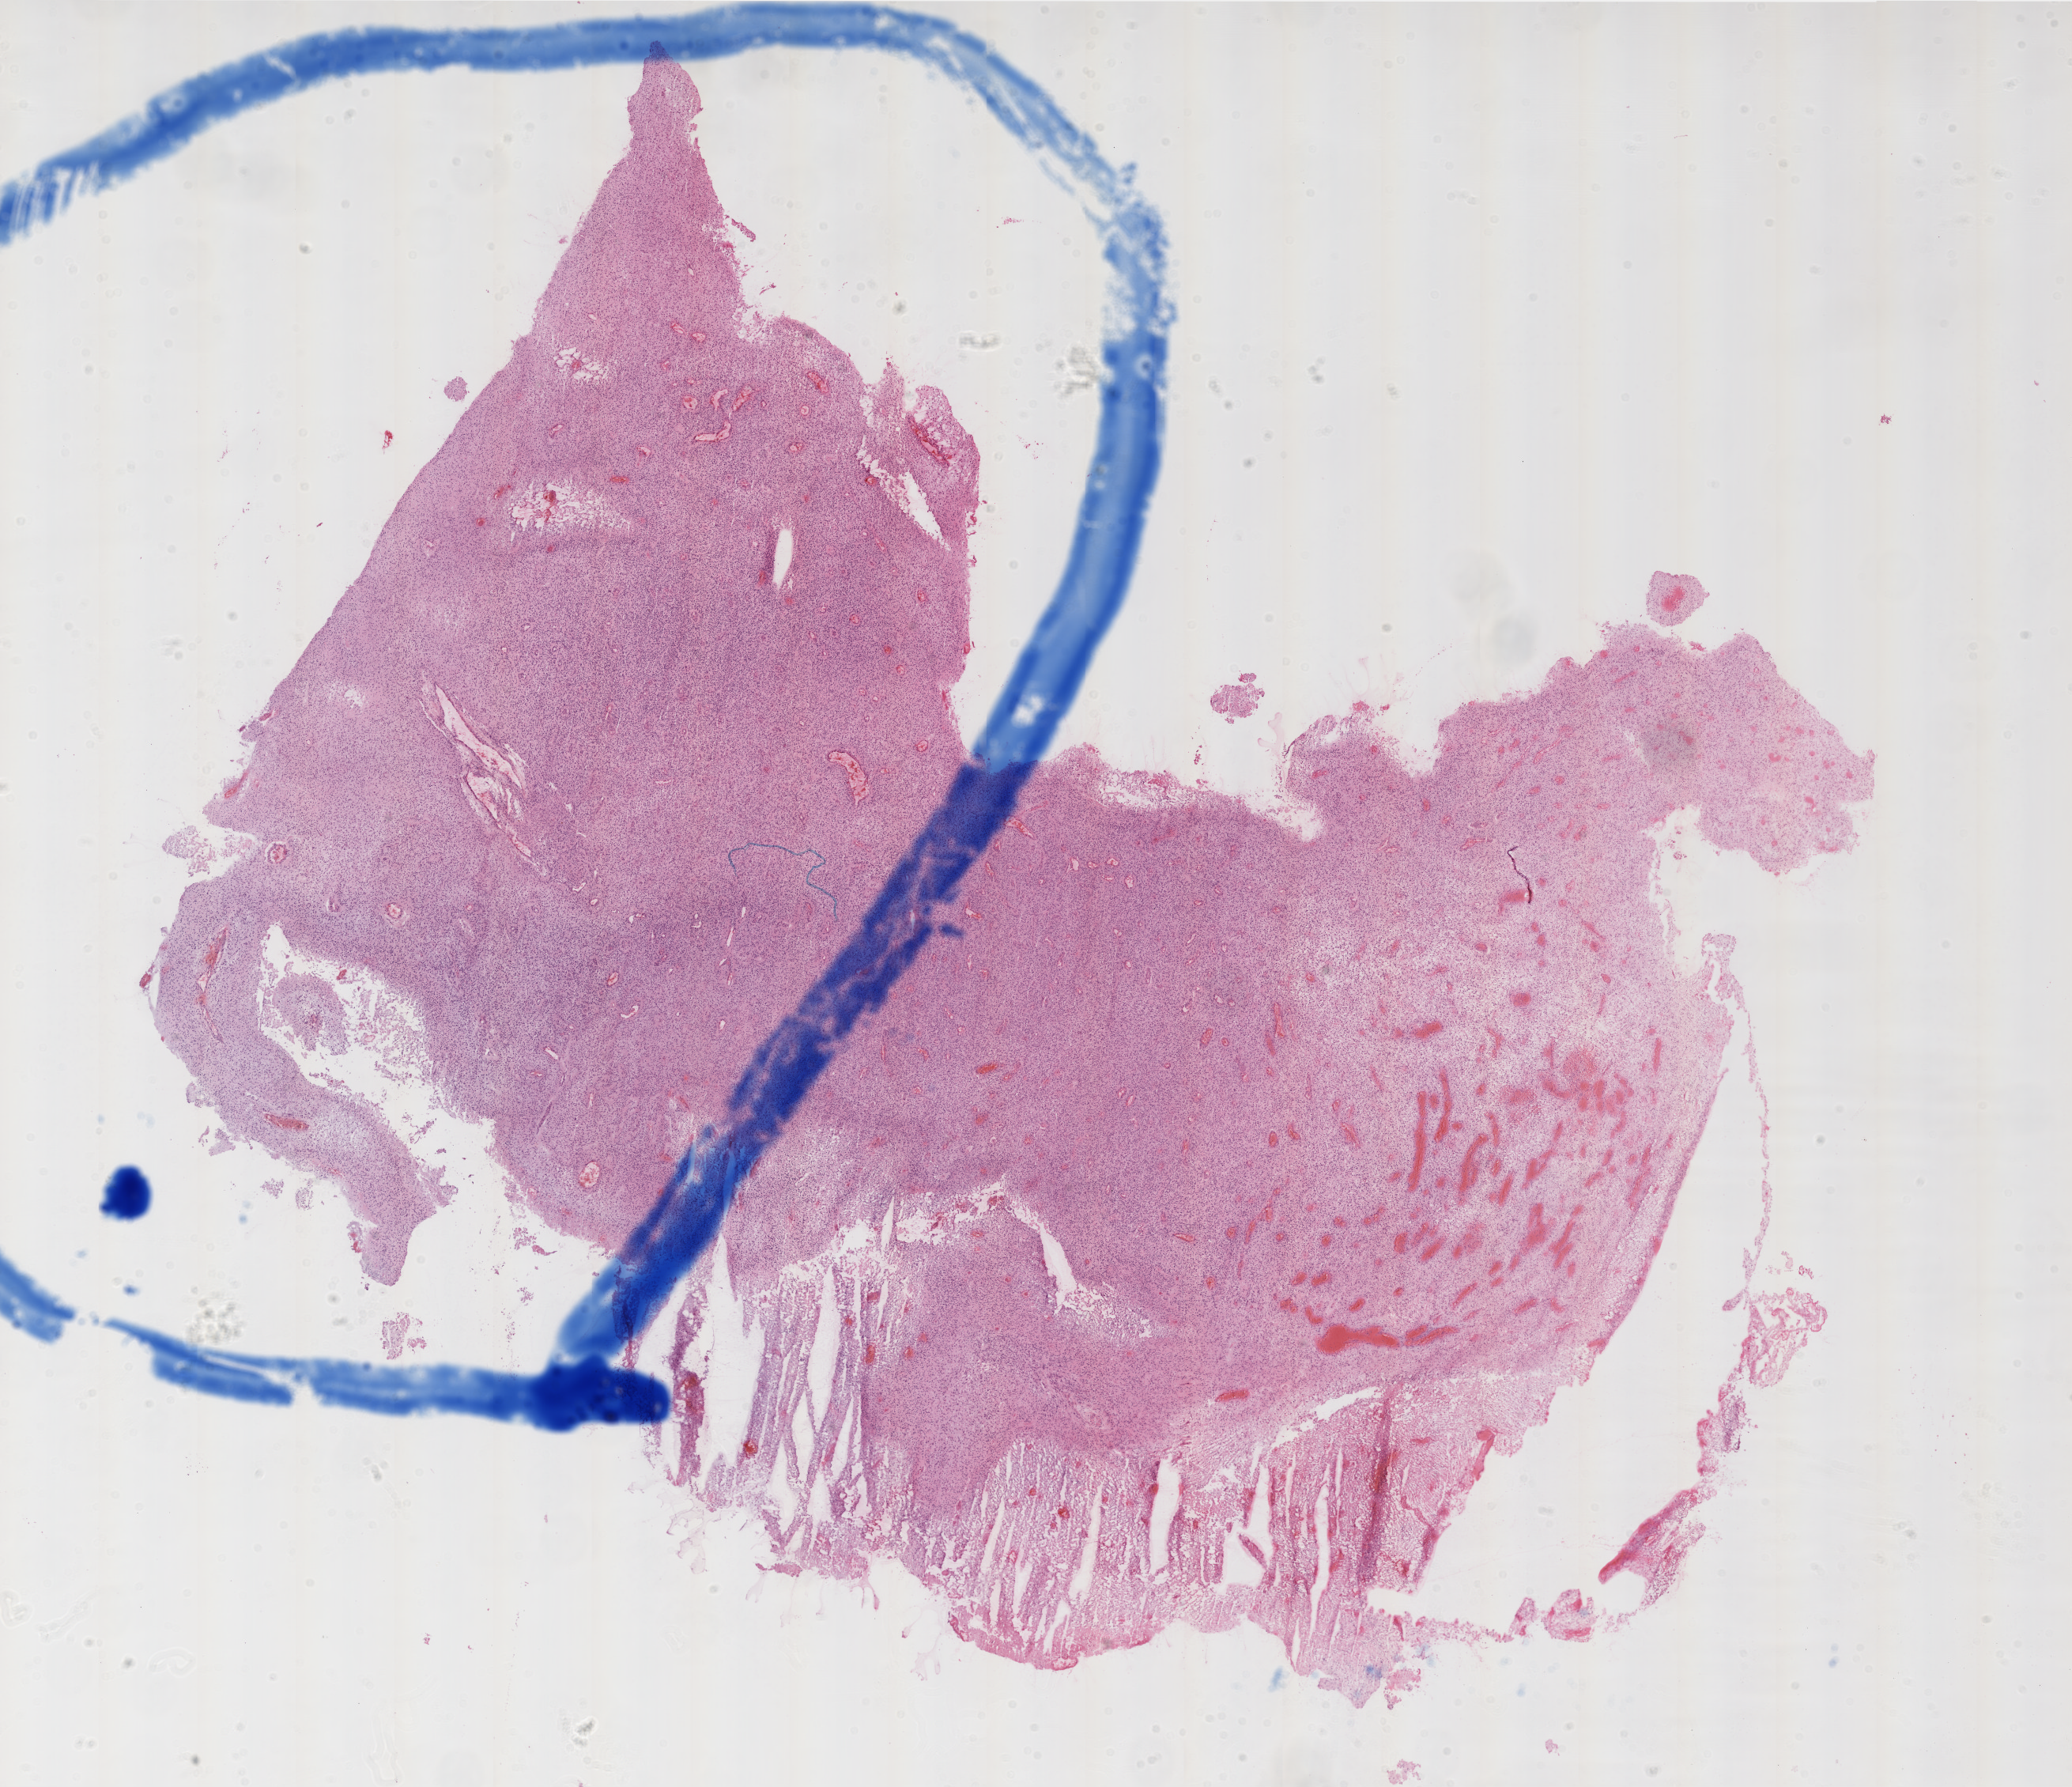
Whole-slide histology image, H&E-stained — a low-resolution overview of the entire scanned area, about 21.0 x 18.1 mm, frozen section from the top of the tissue portion, primary tumour sample from the brain. Patient: female, age at initial diagnosis 74 years. Composition of this section per pathologist review: tumour cells 80%, tumour nuclei 100%, normal cells 0%, stromal cells 0%, necrosis 20%.
Histologic diagnosis: Glioblastoma.